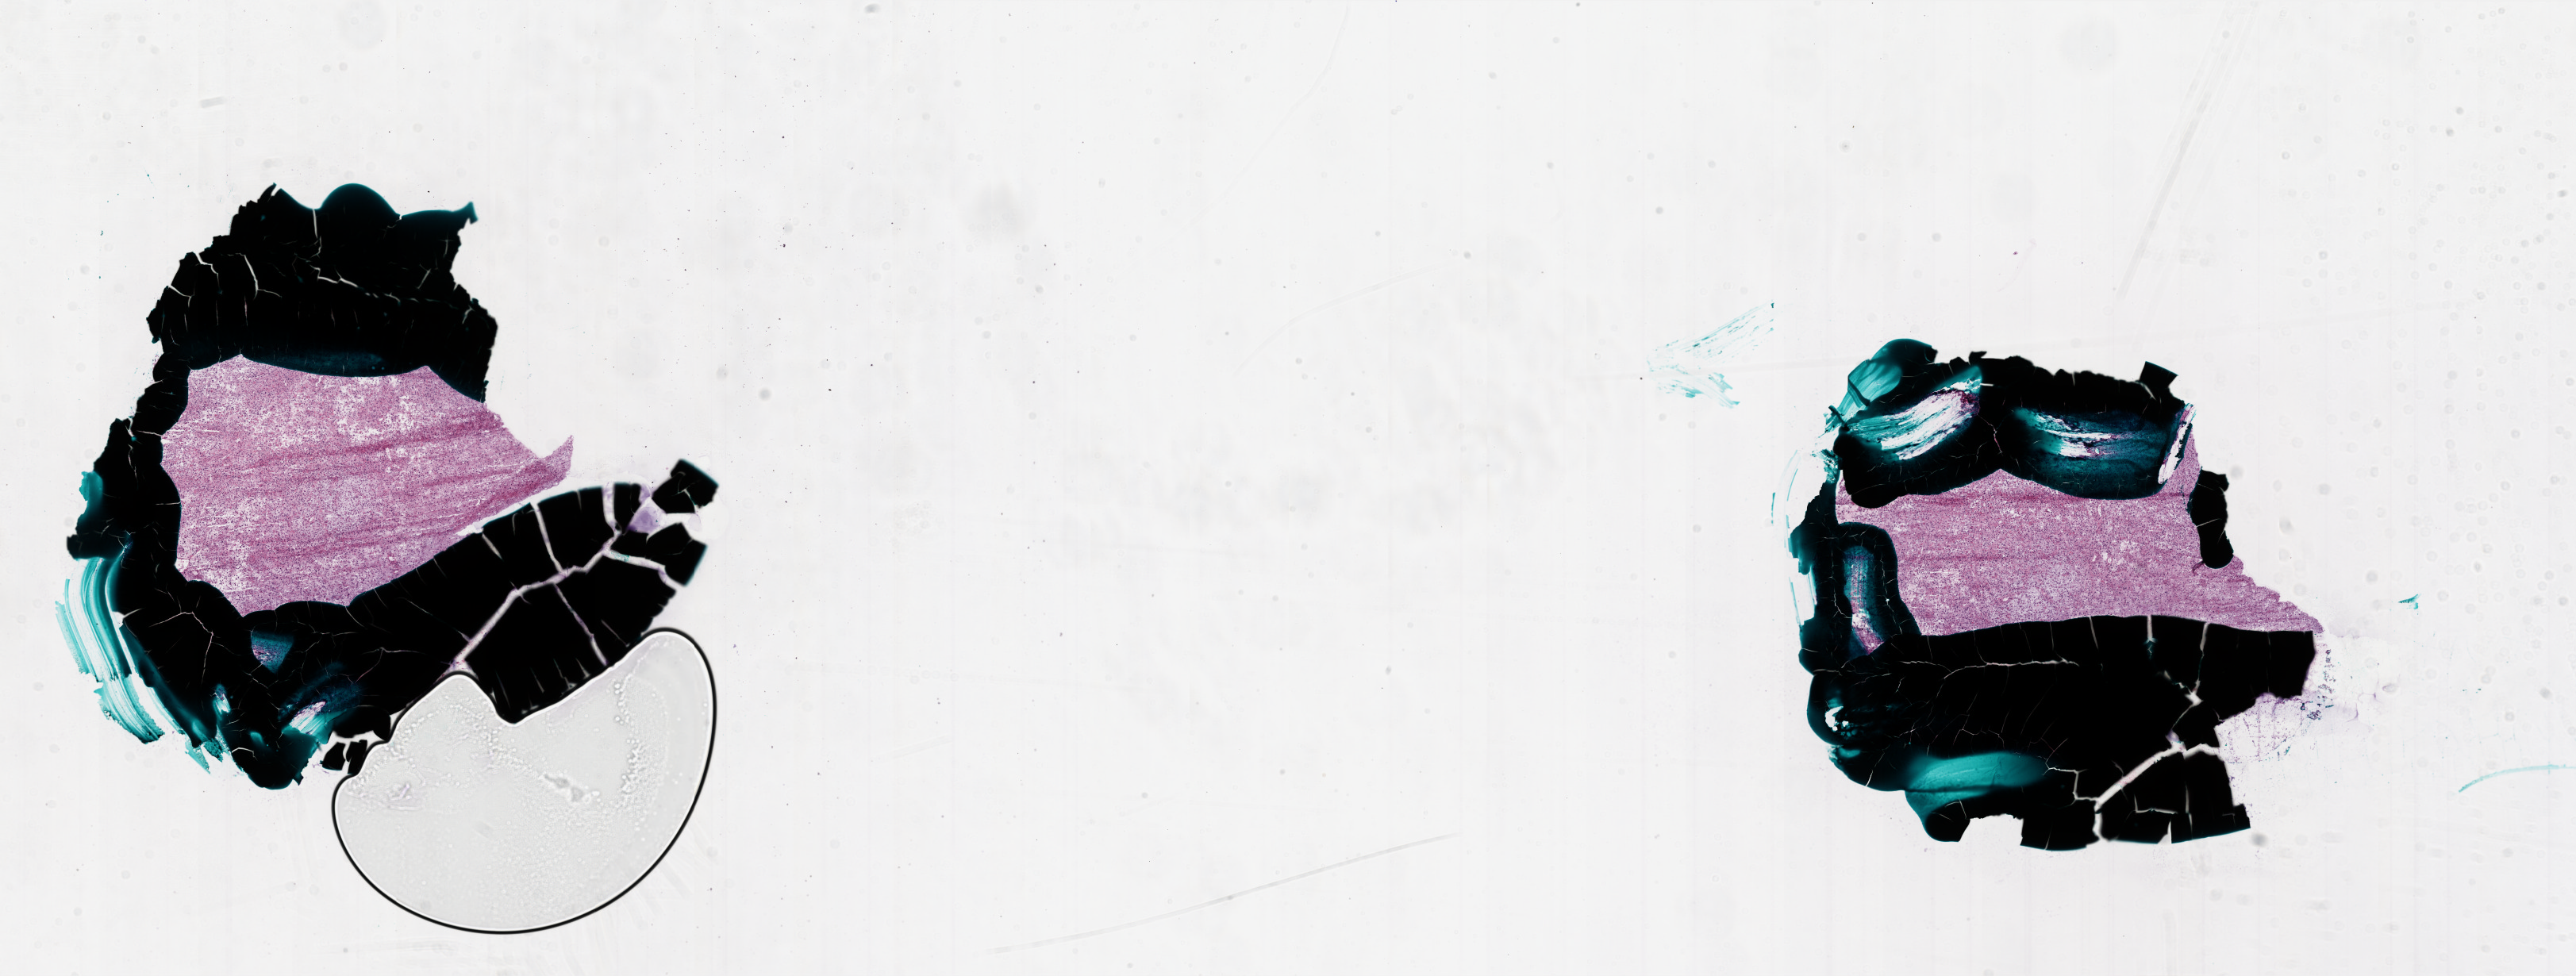
H&E-stained whole-slide image — a low-resolution overview of the entire scanned area, about 26.0 x 9.8 mm (from a 20x scan), frozen section, primary tumour sample from the brain. Male patient; age at initial diagnosis 57 years.
Histologic diagnosis: Glioblastoma.